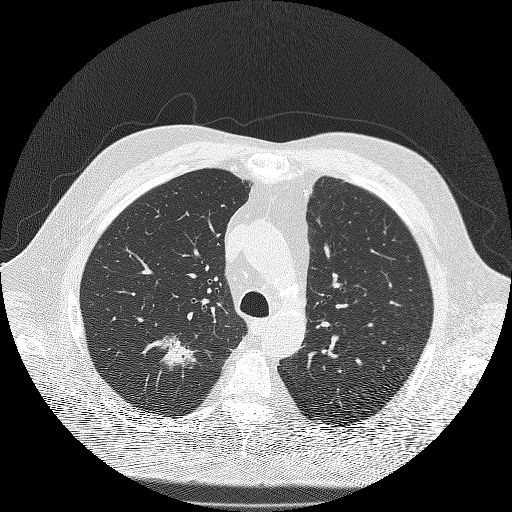
Low-dose screening chest CT, axial slice; second screening round (one year after baseline); lung window (W 1500 / L -600 HU). Male participant, aged 71 years at enrolment.
- Expert reader's lesion annotation, bounding box <136,325,207,389> (left, top, right, bottom; pixels).
- The screening reader recorded 3 non-calcified nodules or masses ≥4 mm on this exam (right upper lobe, right upper lobe, right lower lobe); which of them this box marks is not recorded.
- Official screen result: positive, other.
- Later outcome: lung cancer diagnosed 59 days after this screen — bronchiolo-alveolar adenocarcinoma, NOS, right upper lobe, moderately differentiated (G2), stage IIIA (AJCC 6th edition), 25 mm at pathology.